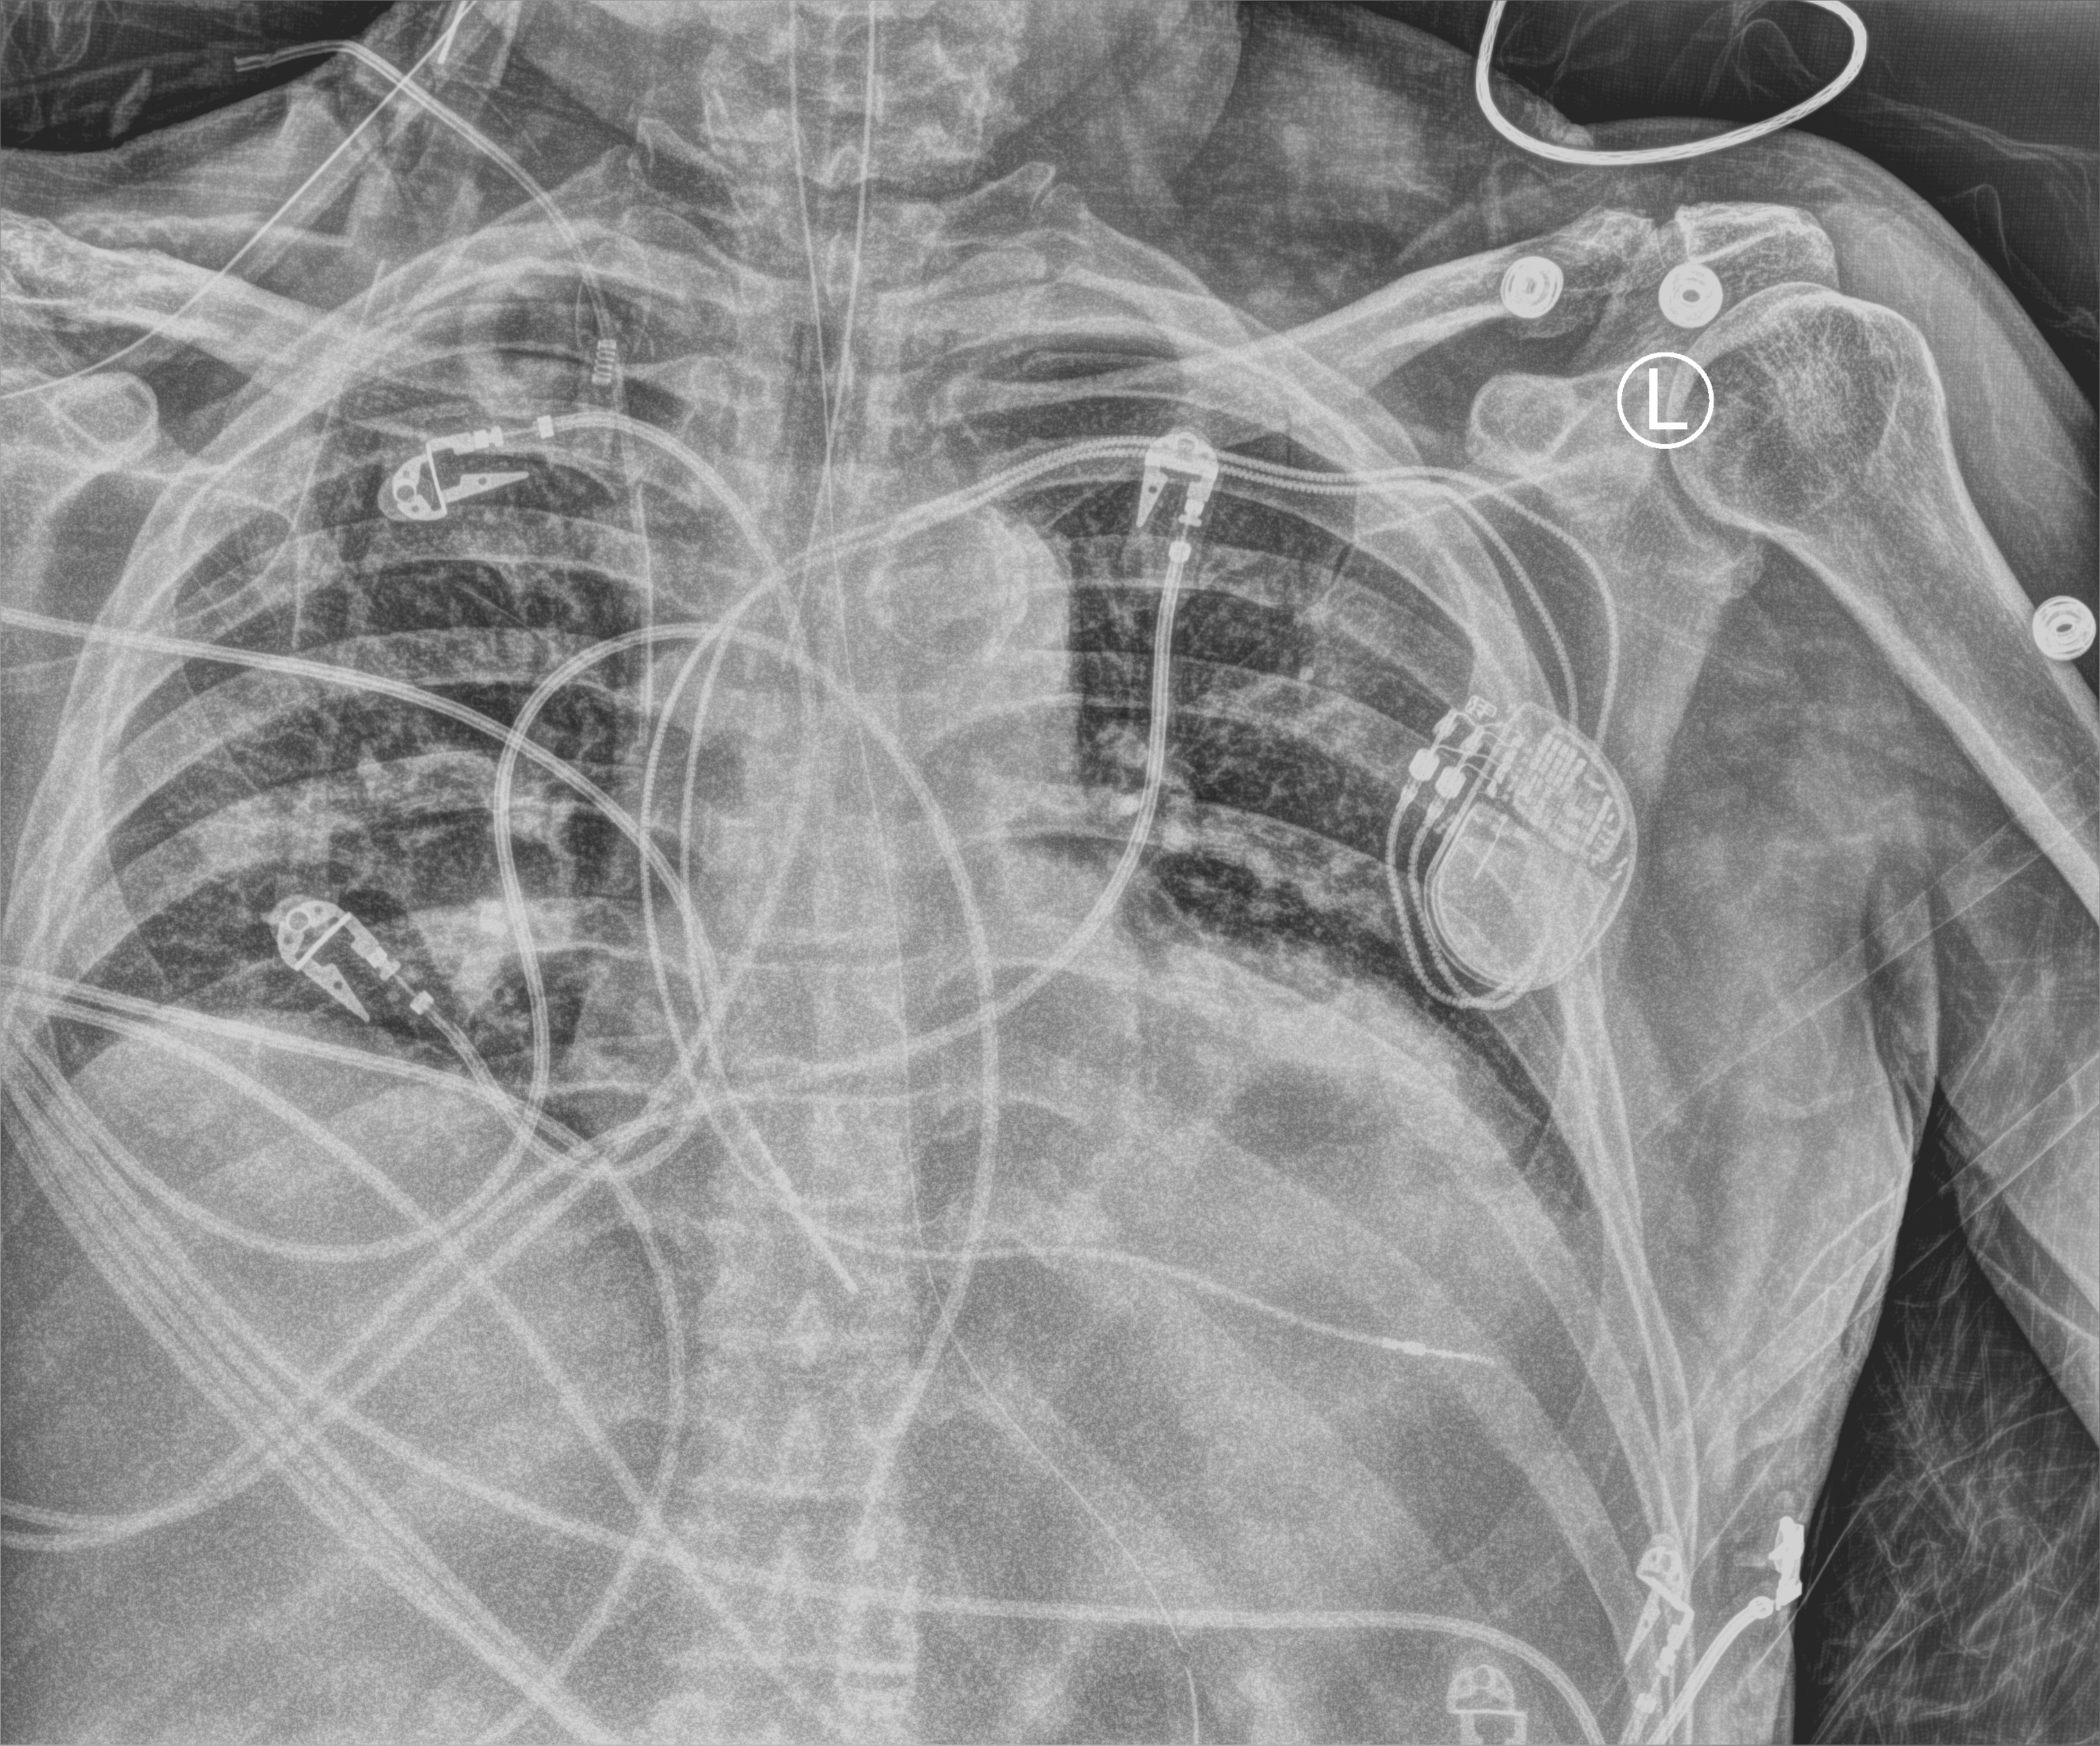
Chest X-ray (portable); anteroposterior (AP) projection. Patient hospitalised with COVID-19; male, aged 60–74 years.
Hospital-stay facts (about this admission, not read from this image; timing relative to this image not recorded): mechanically ventilated during this hospital stay: yes; admitted to intensive care during this hospital stay: yes.